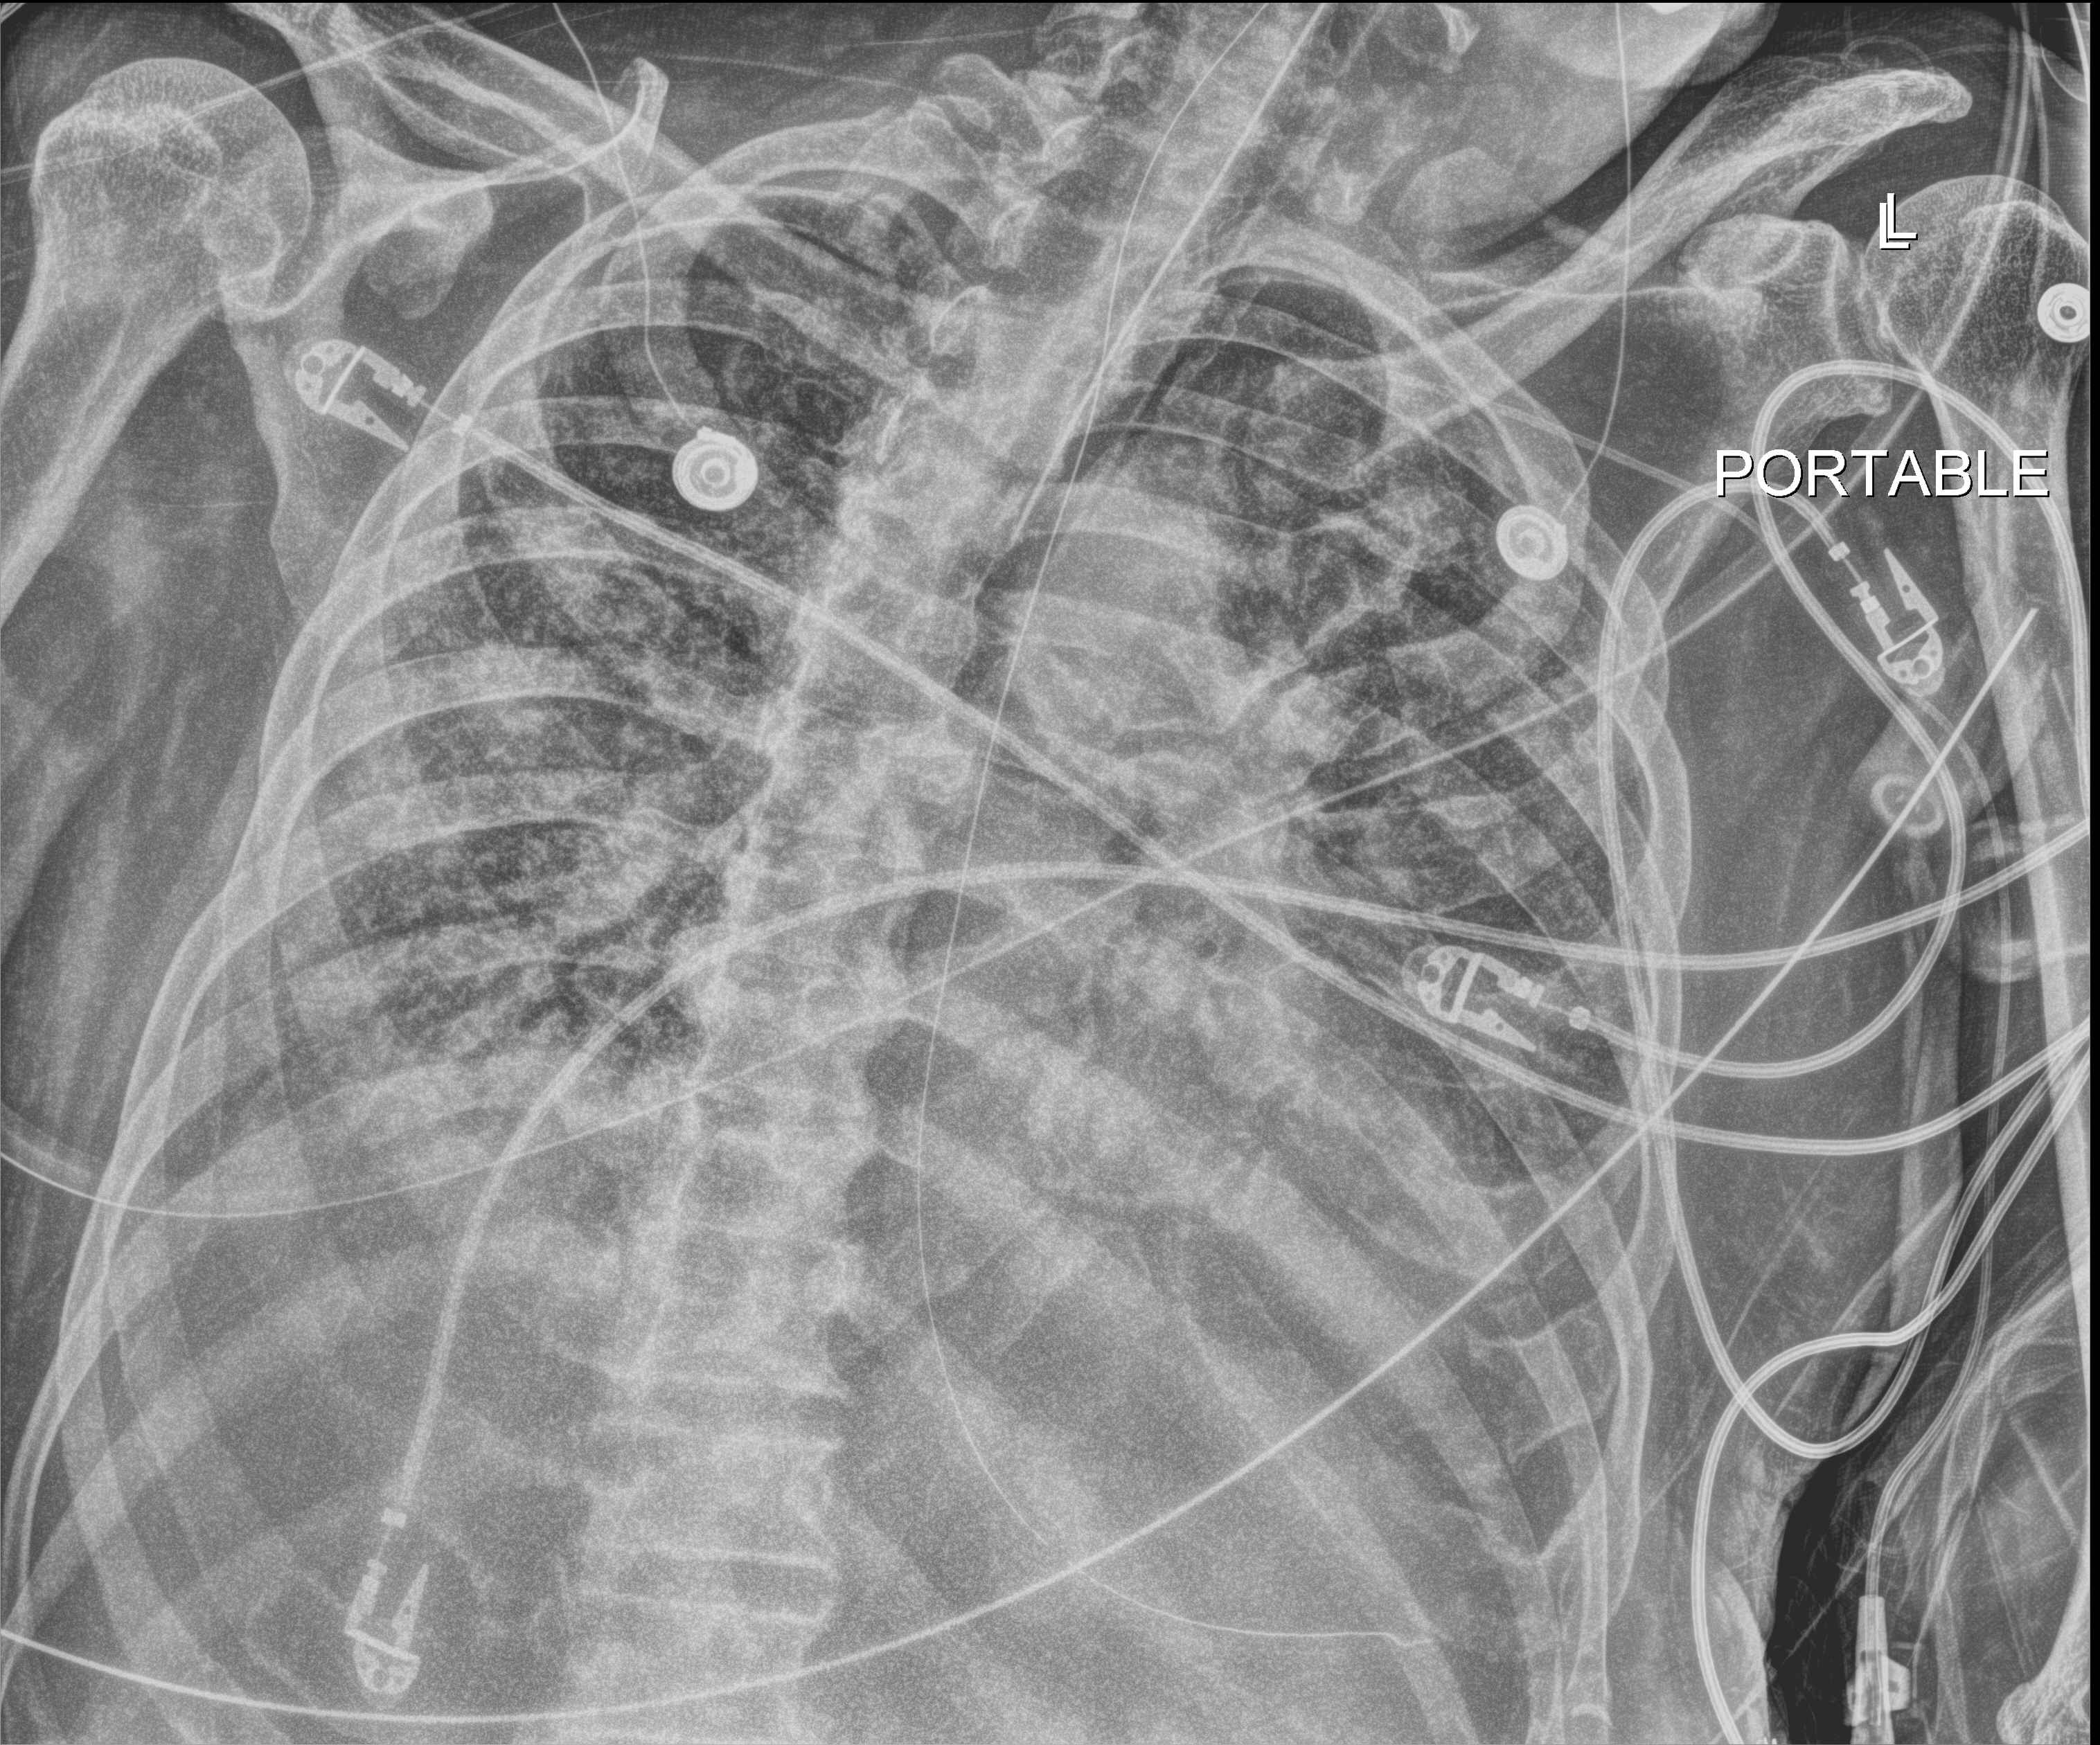
Chest X-ray (portable); anteroposterior (AP) projection. Male patient hospitalised with COVID-19, age 75–90 years.
From the hospital-stay record, not from the radiograph (when in the stay this image was taken is not recorded): length of hospital stay: 33 days; admitted to intensive care during this hospital stay: yes; COPD (admission record): no.